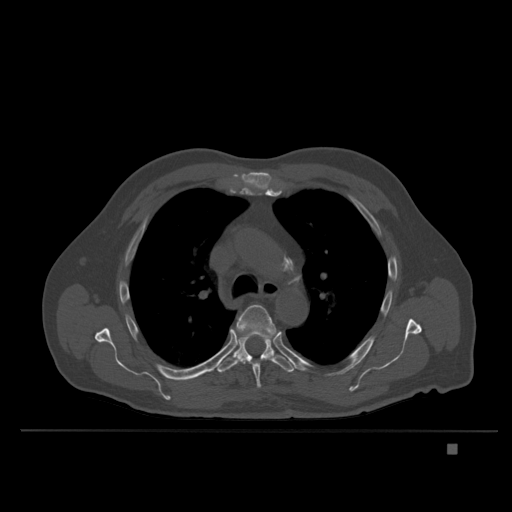
CT including the spine, one axial slice; slice 267 of 435 in the series (ordered by position); bone window (W 1800 / L 400 HU); 512 × 512 image matrix, field of view 434 × 434 mm. Male patient, age 73 years. Case-level facts recorded for this patient, not image findings: primary cancer: skin.
Outlined on this slice (semi-automatically segmented with operator editing):
- T5 vertebra: bounding box <235,304,277,388> (left, top, right, bottom; pixels)
- T6 vertebra: <216,333,294,373>
- T7 vertebra: <234,339,238,347>